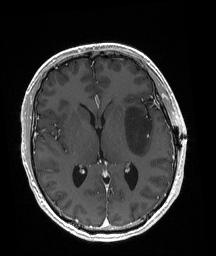
Brain MRI from a brain-tumour surgery series, one axial slice. Slice 98 of 192 in the series (ordered by position). T1-weighted post-contrast. 216 × 256 image matrix, field of view 211 × 250 mm. Case-level facts recorded for this patient, not image findings: histopathology: Astrocytoma; WHO grade: 3; IDH mutation: yes; tumour location: Left Posterior Frontal.
Annotated regions visible in this slice (manually delineated by an expert):
- tumour: bounding box [x1, y1, x2, y2] px = [124, 106, 152, 157]